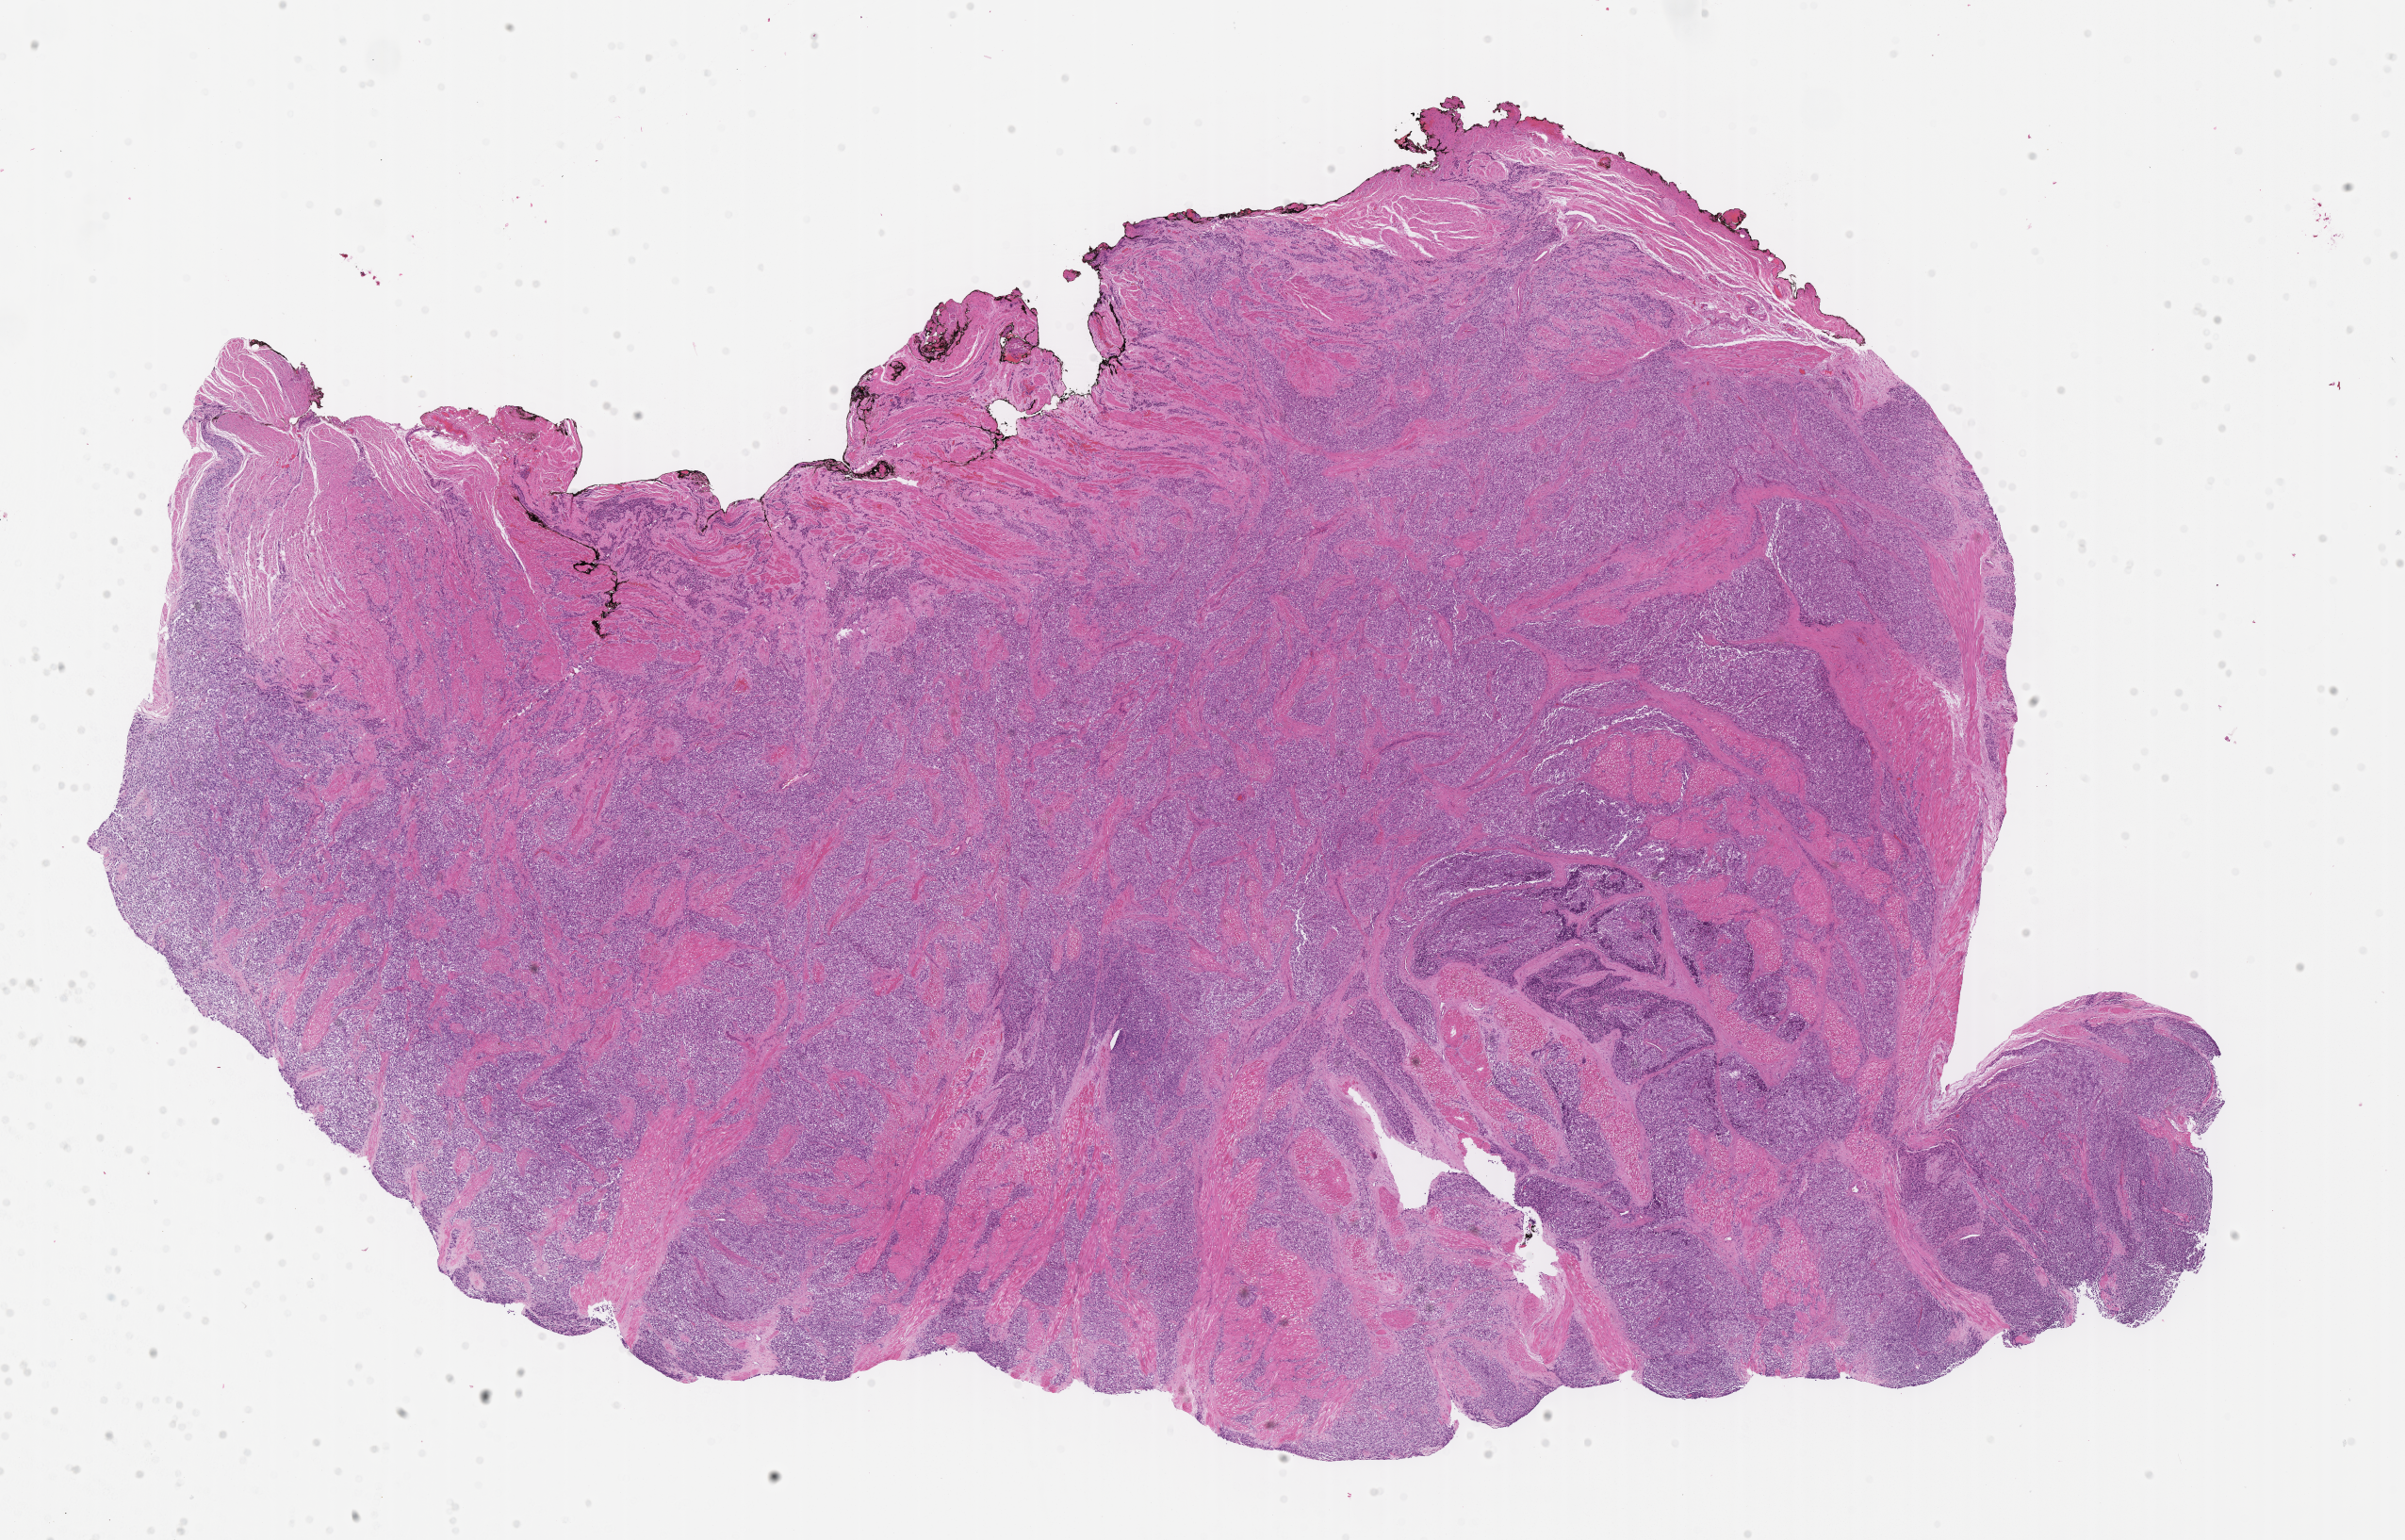
Digitized H&E-stained section of tumor tissue, shown as a low-resolution overview of the whole scanned area (about 20.6 x 13.2 mm). FFPE section. Site: perianal, right. Male patient, age at diagnosis 8.3 years.
Diagnosis: rhabdomyosarcoma; histological classification: alveolar rhabdomyosarcoma.